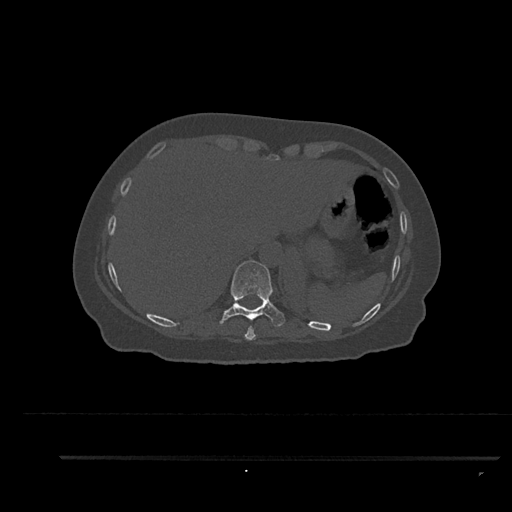
CT including the spine, one axial slice; position 368 of 797 along the scan axis; reconstruction kernel Br40s/3; bone window (W 1800 / L 400 HU); 0.5 mm slice thickness; 512 × 512 image matrix, field of view 408 × 408 mm. Female patient, age 44 years. From the clinical record (not read from this slice): primary cancer: renal; vertebrae with lytic lesions (as recorded): L1.
Outlined on this slice (semi-automatic segmentation, software-assisted and operator-edited):
- T10 vertebra: bounding box (x1, y1, x2, y2) in pixels: (220, 260, 286, 331)
- T9 vertebra: (244, 328, 256, 340)